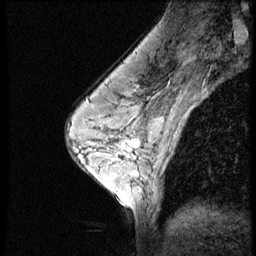
Breast MRI (dynamic contrast-enhanced), one sagittal slice. Slice 34 of 52 in the series (ordered by position). 3 images stored at this slice position (order not interpretable as contrast timing). 1.5 T. TE 4.2 ms, TR 9 ms. 2.5 mm slice thickness. 256 × 256 image matrix. Patient: female, 50 years. Case-level facts recorded for this patient, not image findings: setting: breast cancer imaged before/during neoadjuvant chemotherapy; receptor status: HR-positive, HER2-negative.
Outlined on this slice (semi-automatic segmentation, software-assisted and operator-edited):
- analysis volume of interest (the breast-tissue region the enhancement analysis was run in; not a lesion): bounding box <103,130,151,181> (left, top, right, bottom; pixels)
- tumour enhancement mask (voxels above the 140 % enhancement threshold inside the analysis volume of interest): <132,140,139,147>